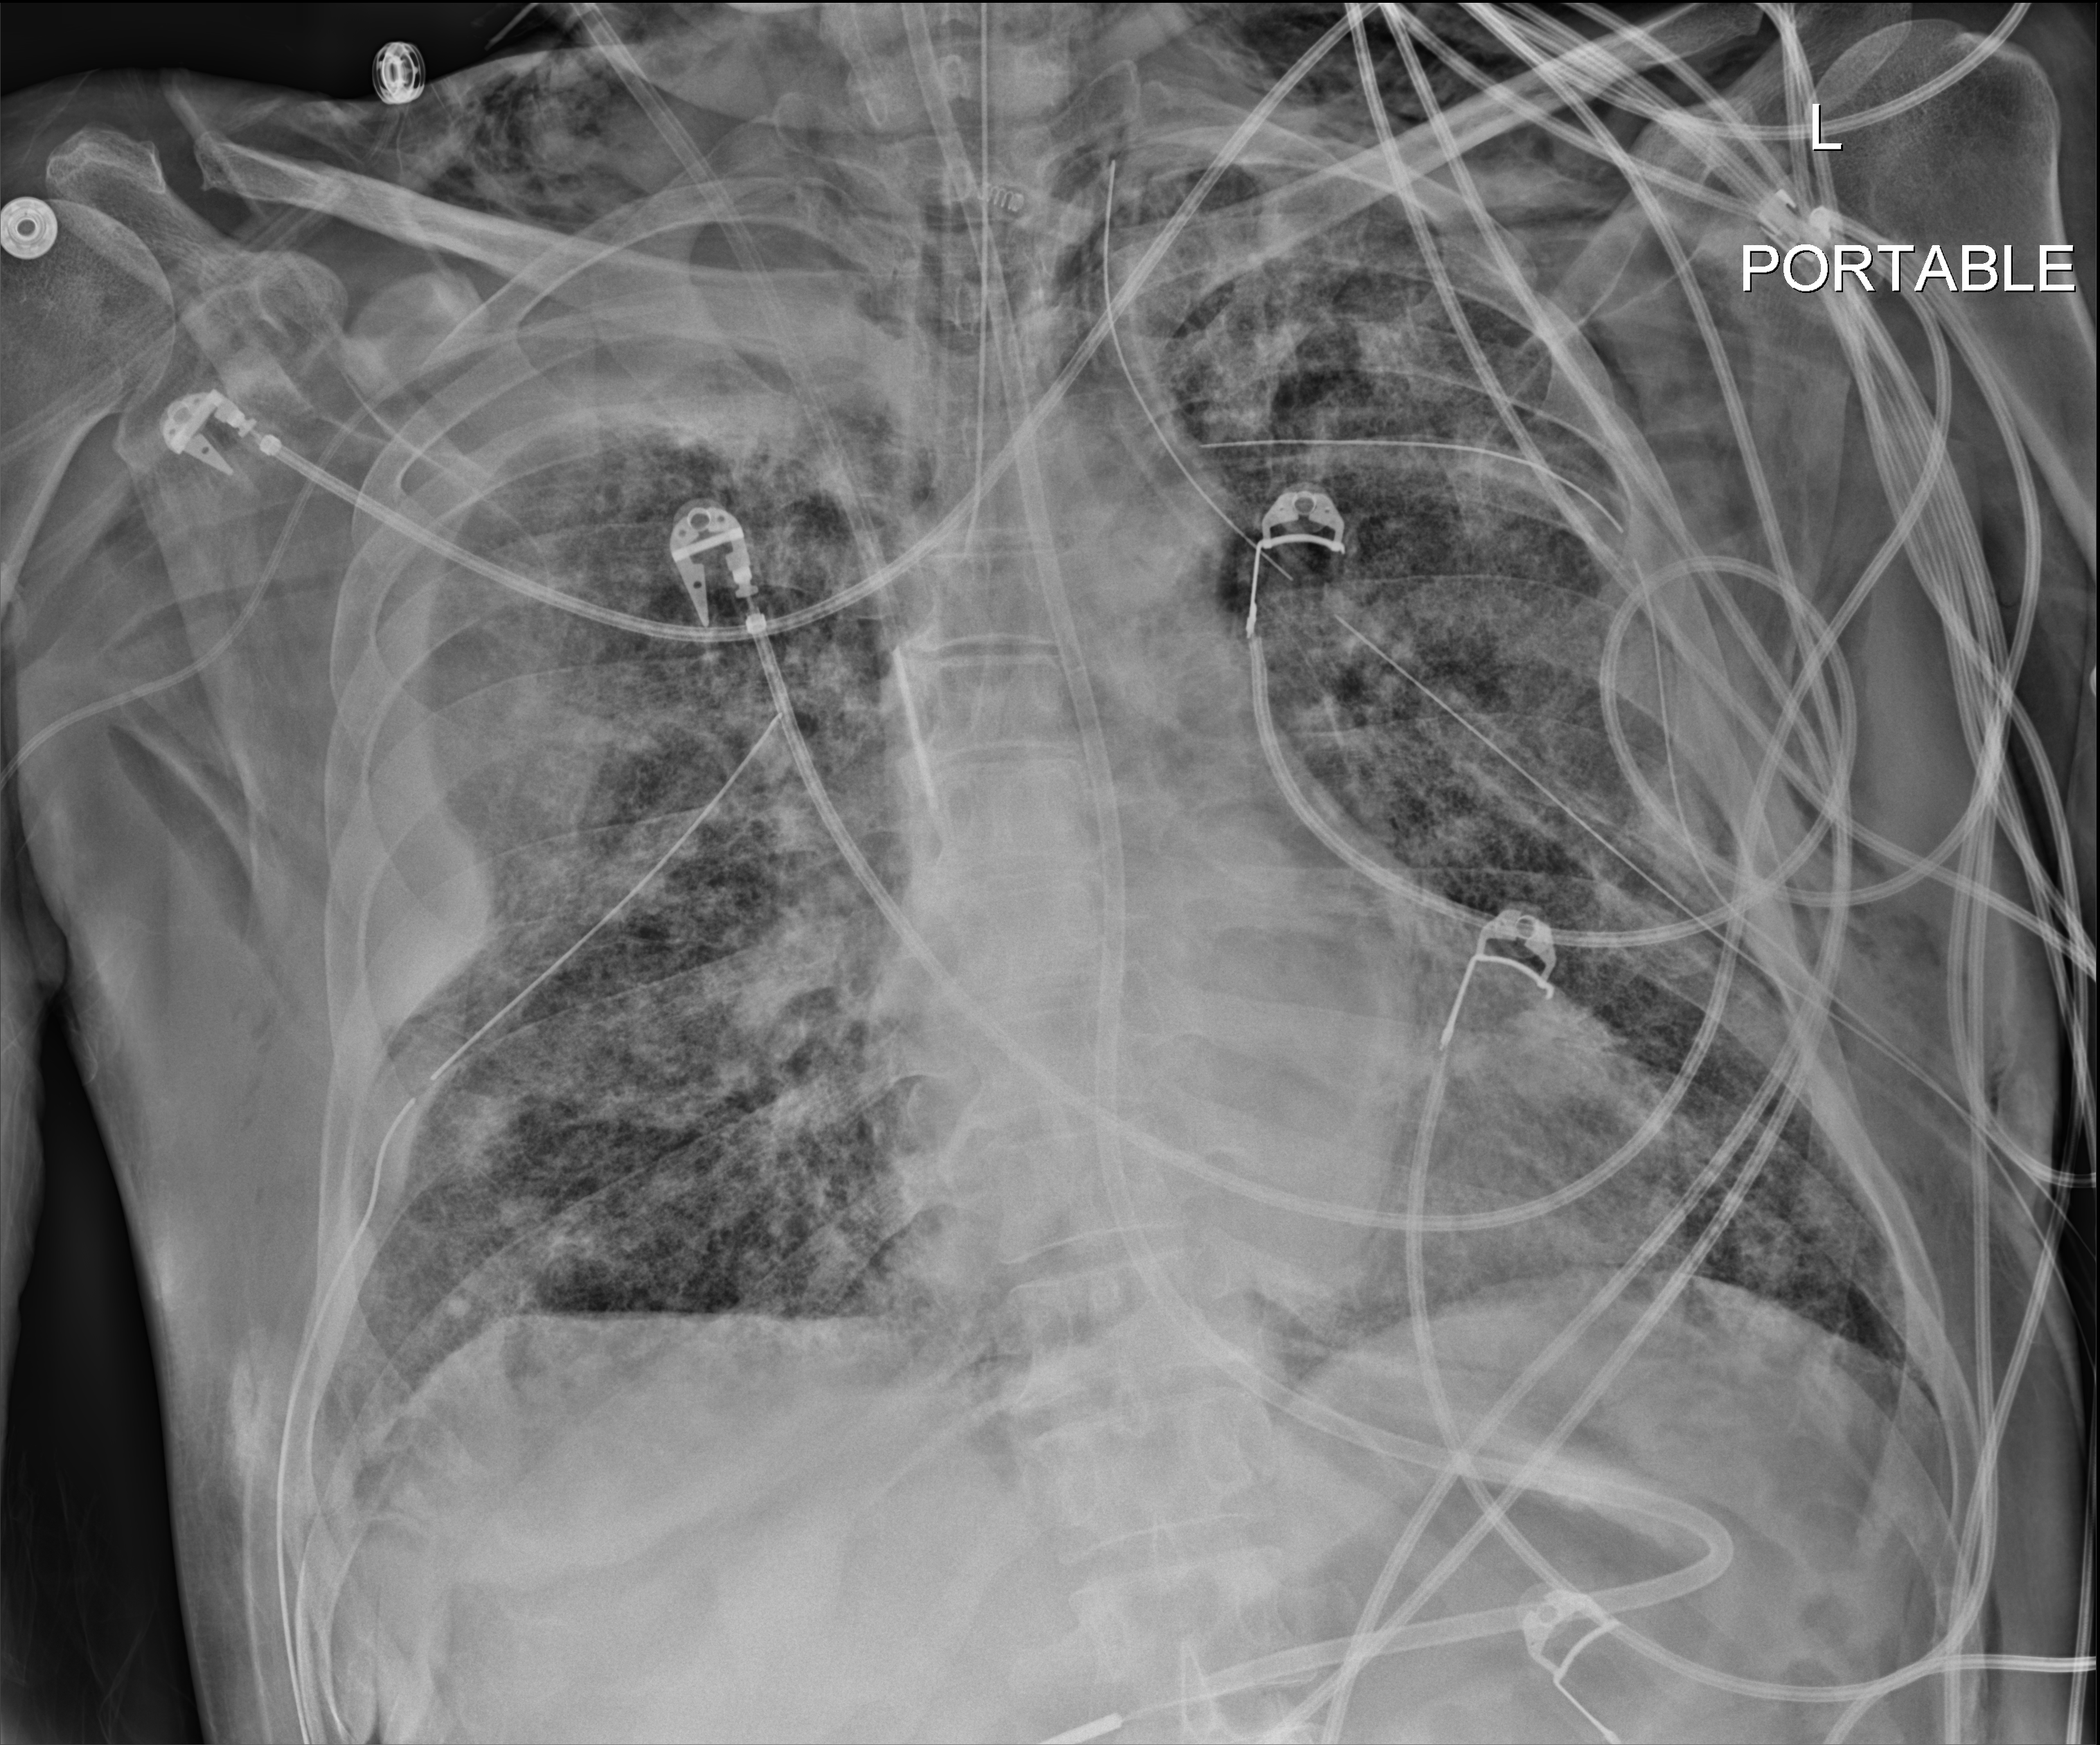
Chest X-ray (portable); anteroposterior (AP) projection. Male patient hospitalised with COVID-19, age 18–59 years.
Admission-level facts for this patient (not findings on this image; timing relative to this image not recorded): diabetes (admission record): no; chronic kidney disease (admission record): no; admitted to intensive care during this hospital stay: yes.